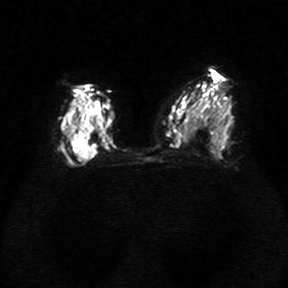
Breast MRI, one axial slice. Diffusion-weighted series; image 2 of 4 stored at this slice position (different b-values; order by instance number). 1.5 T. 288 × 288 image matrix, field of view 340 × 340 mm. Female patient.
Structures marked on this image (manually delineated by an expert):
- tumour on diffusion-weighted imaging: bounding box (x1, y1, x2, y2) in pixels: (67, 127, 94, 162)